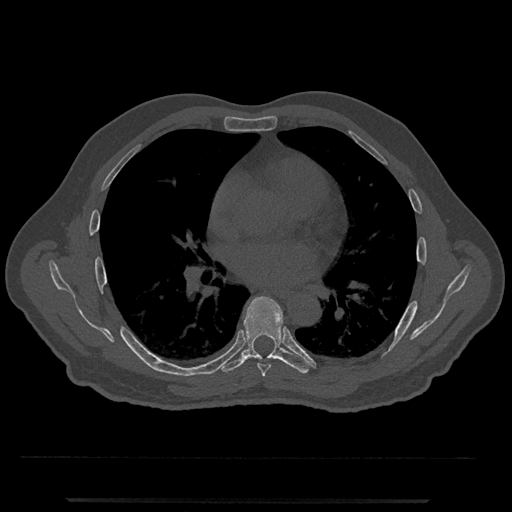
CT including the spine, one axial slice. Position 705 of 797 along the scan axis. Reconstruction kernel Br40s/3. 120 kVp. Bone window (W 1800 / L 400 HU). 0.5 mm slice thickness. 512 × 512 image matrix, field of view 419 × 419 mm. Male patient, age 63 years. From the clinical record (not read from this slice): primary cancer: prostate.
Structures marked on this image (semi-automatic segmentation, software-assisted and operator-edited):
- T6 vertebra: bounding box <257,363,271,377> (left, top, right, bottom; pixels)
- T7 vertebra: <219,296,310,374>